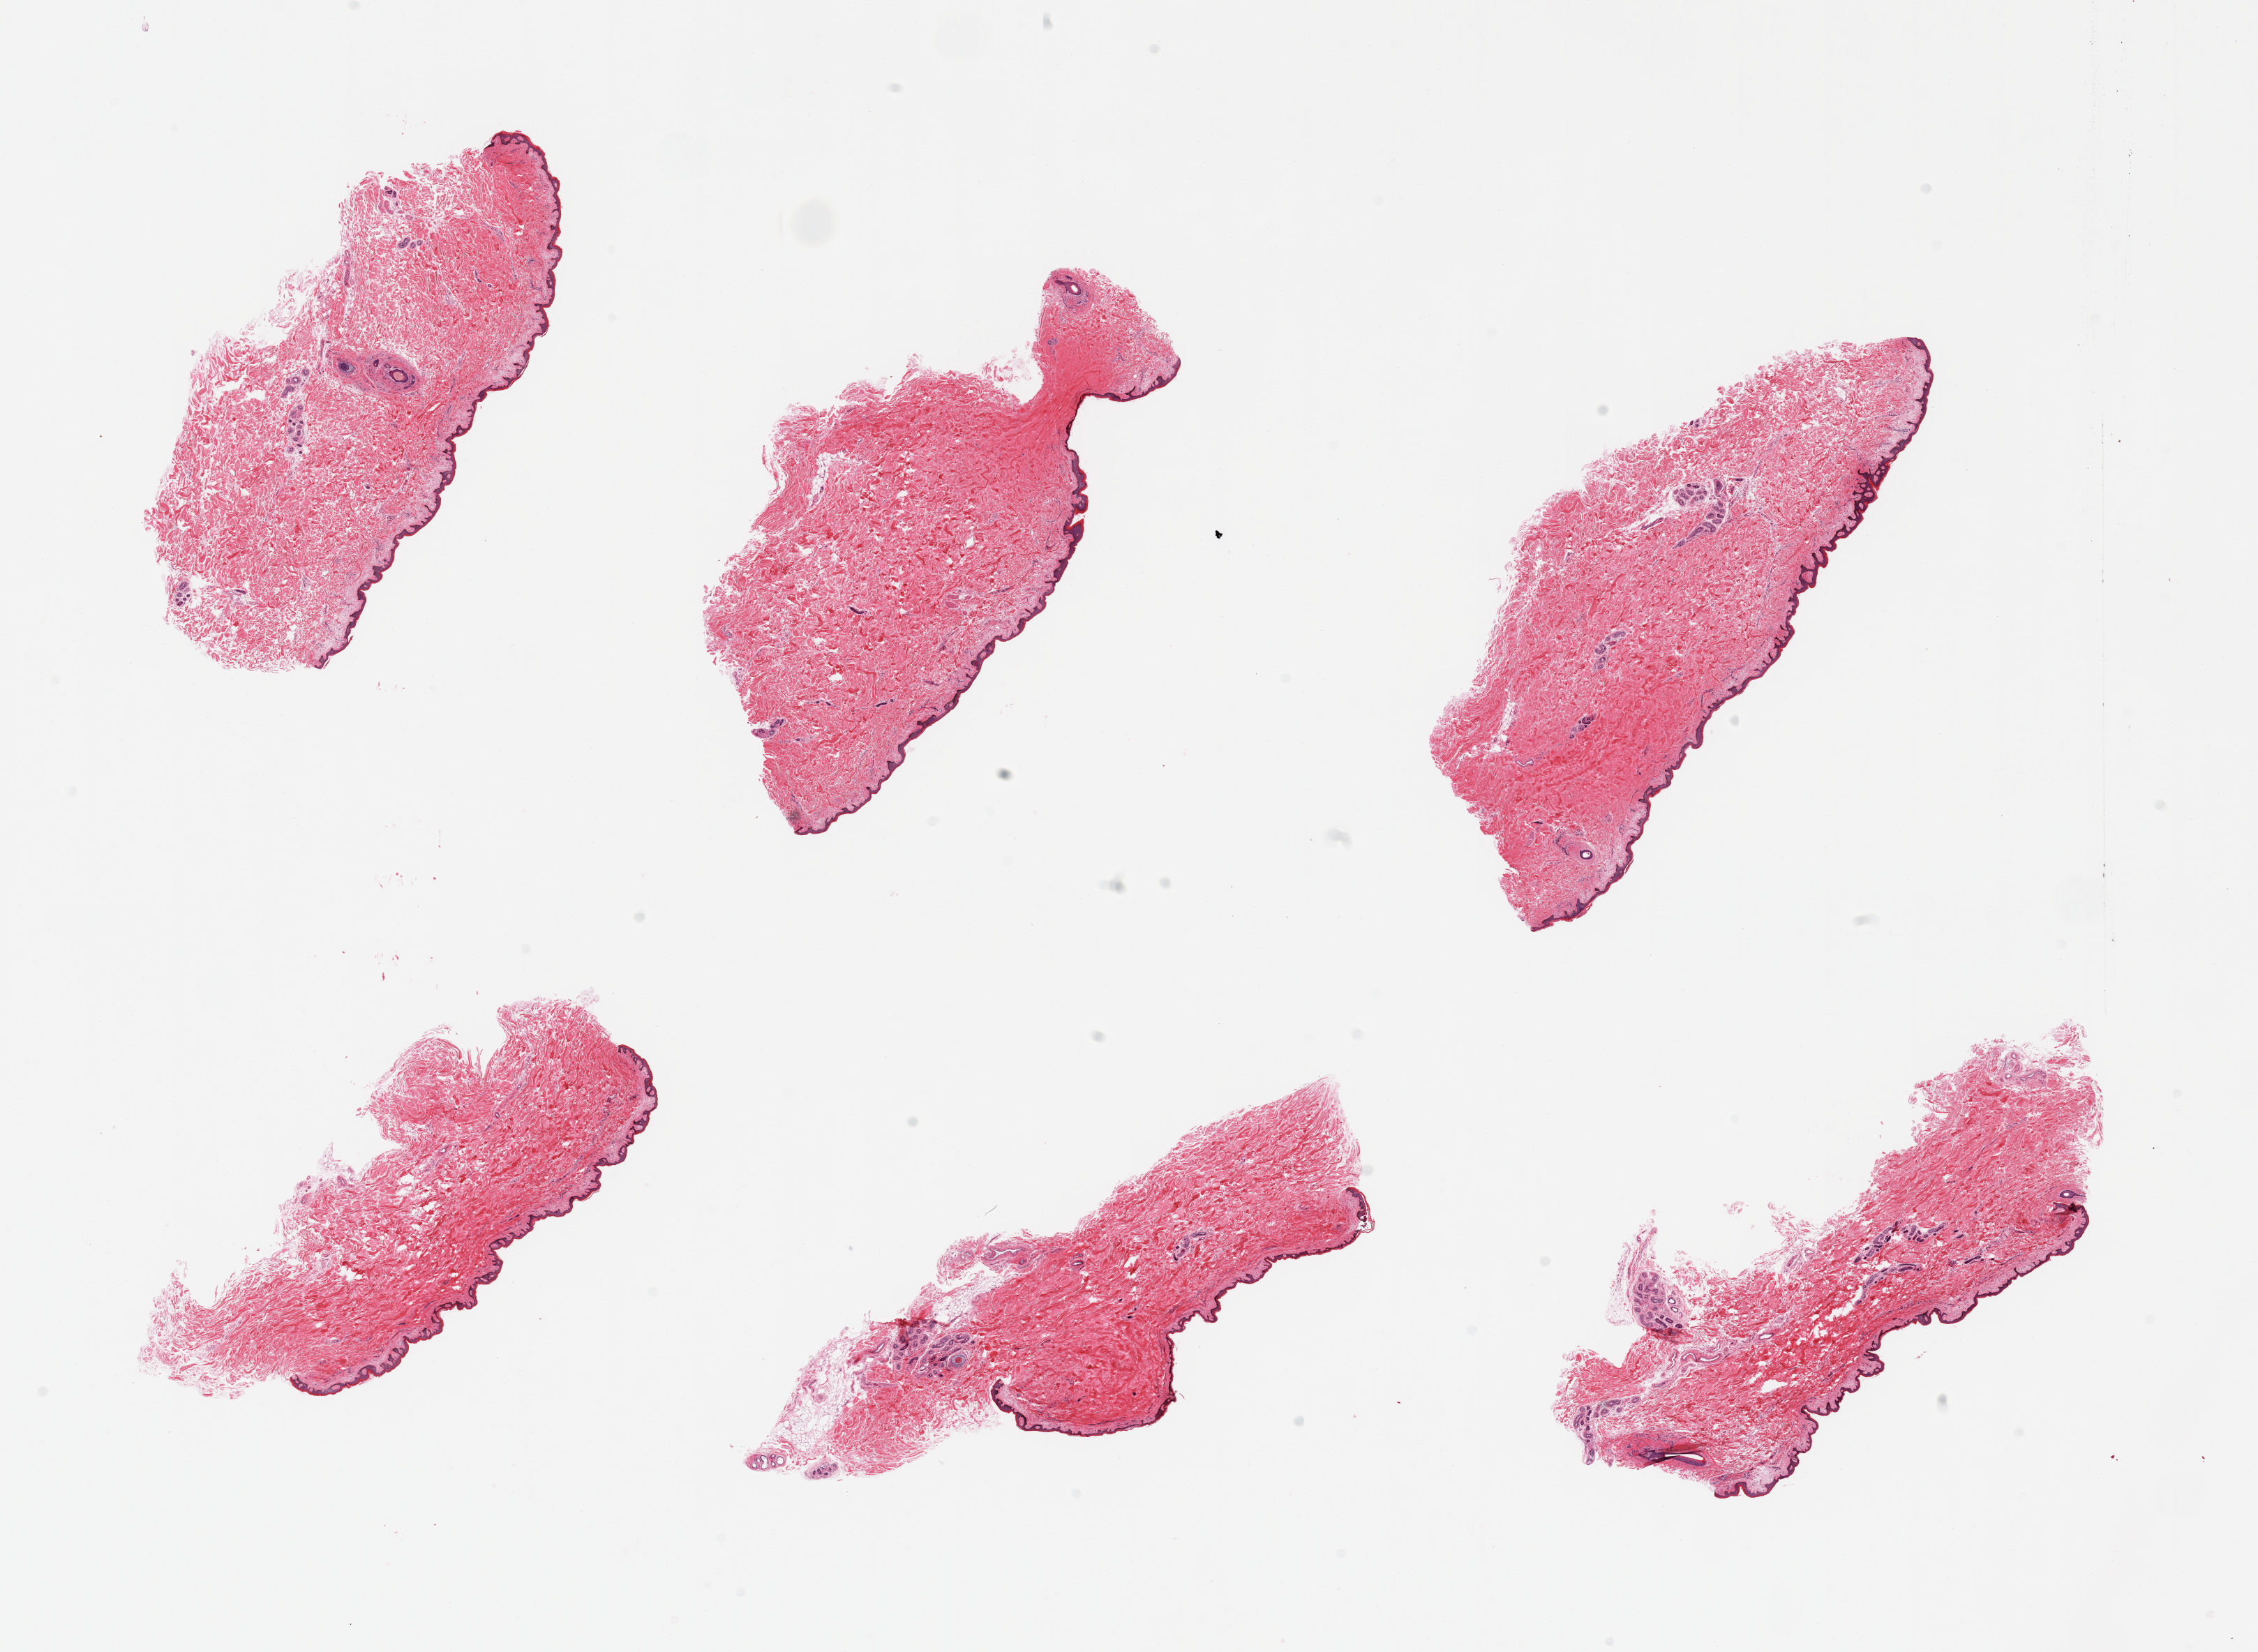
Whole-slide image, H&E stain, low-resolution overview of the scanned area, about 25.6 x 18.7 mm (acquisition: 20x scan). PAXgene-fixed, paraffin-embedded tissue. Section of skin of suprapubic region (target tissue). Tissue donor sample. Male donor.
Review note (as recorded): 6 pieces, minimal dermal fat. Squamous epithelium is ~70 microns.